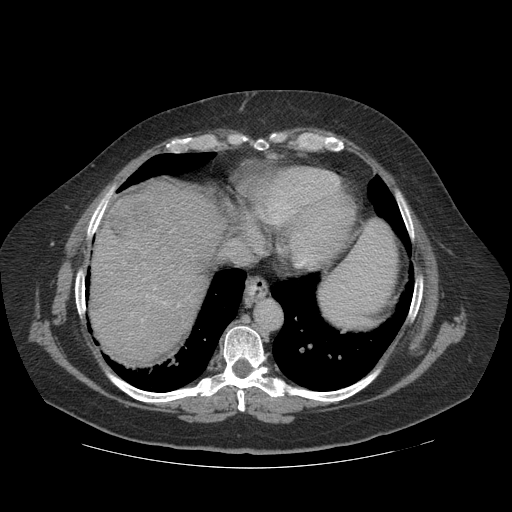
Contrast-enhanced abdominal CT (liver protocol), one axial slice; slice 101 of 121 in the series (ordered by position); 140 kVp; soft-tissue window (W 400 / L 40 HU); 2.5 mm slice thickness; 512 × 512 image matrix. Case-level facts recorded for this patient, not image findings: diagnosis: hepatocellular carcinoma (patient treated with transarterial chemoembolisation; whether this scan precedes or follows treatment is not stated here); TNM stage (as recorded): Stage-IIIA; Child-Pugh class: A; tumour differentiation: well differentiated; tumour size: 7.4 cm.
Outlined on this slice (semi-automatic segmentation, software-assisted and operator-edited):
- abdominal aorta: box from (x=257, y=301) to (x=281, y=331) px
- liver parenchyma outside the tumour (the mass and vessels are separate outlines, so this box may not span the whole liver): (x=90, y=180)–(x=228, y=364)
- mass: (x=107, y=195)–(x=154, y=249)
- liver vessels: (x=124, y=272)–(x=181, y=334)